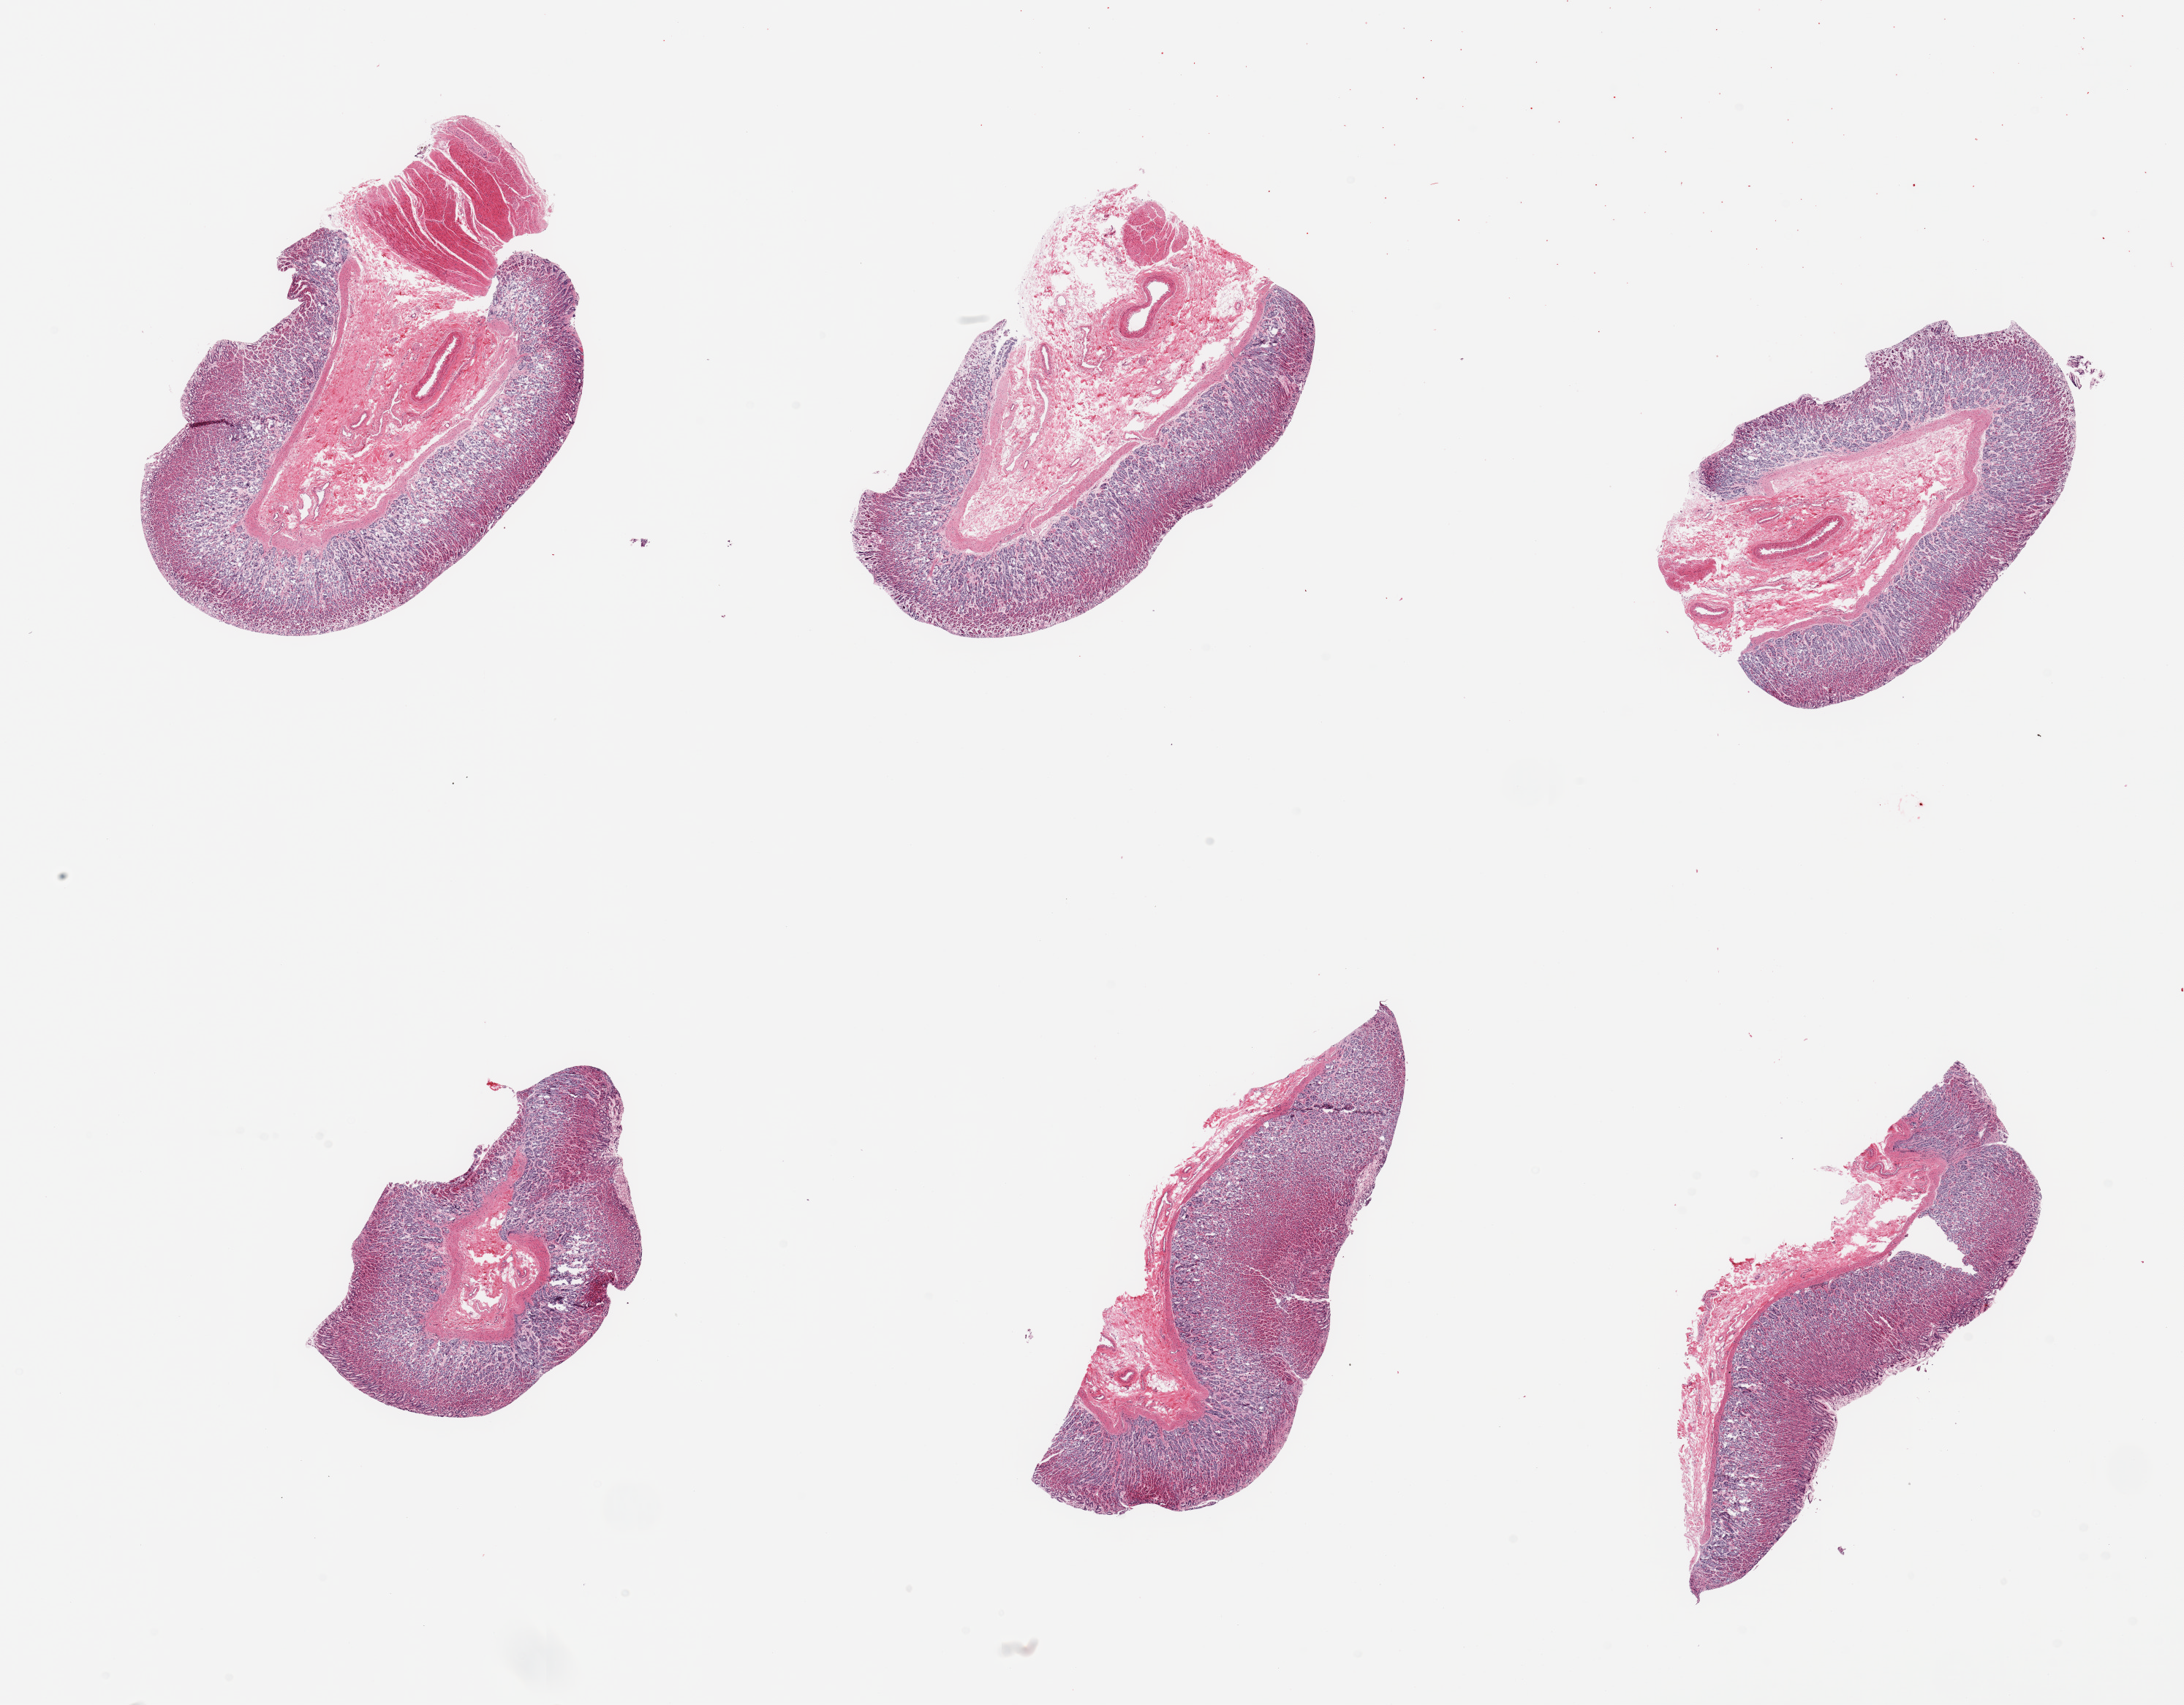
Hematoxylin and eosin (H&E) whole-slide image — whole scanned area (about 23.6 x 18.4 mm, from a 20x scan) shown as a low-resolution overview, PAXgene-fixed paraffin-embedded (PFPE) section, target tissue: stomach, donor tissue sample. Donor sex: male.
- reviewer comment on this tissue sample: 6 pieces; predominanlty mucosa and submucosa, two pieces include portion of muscularis (also target), mild to moderate autolysis